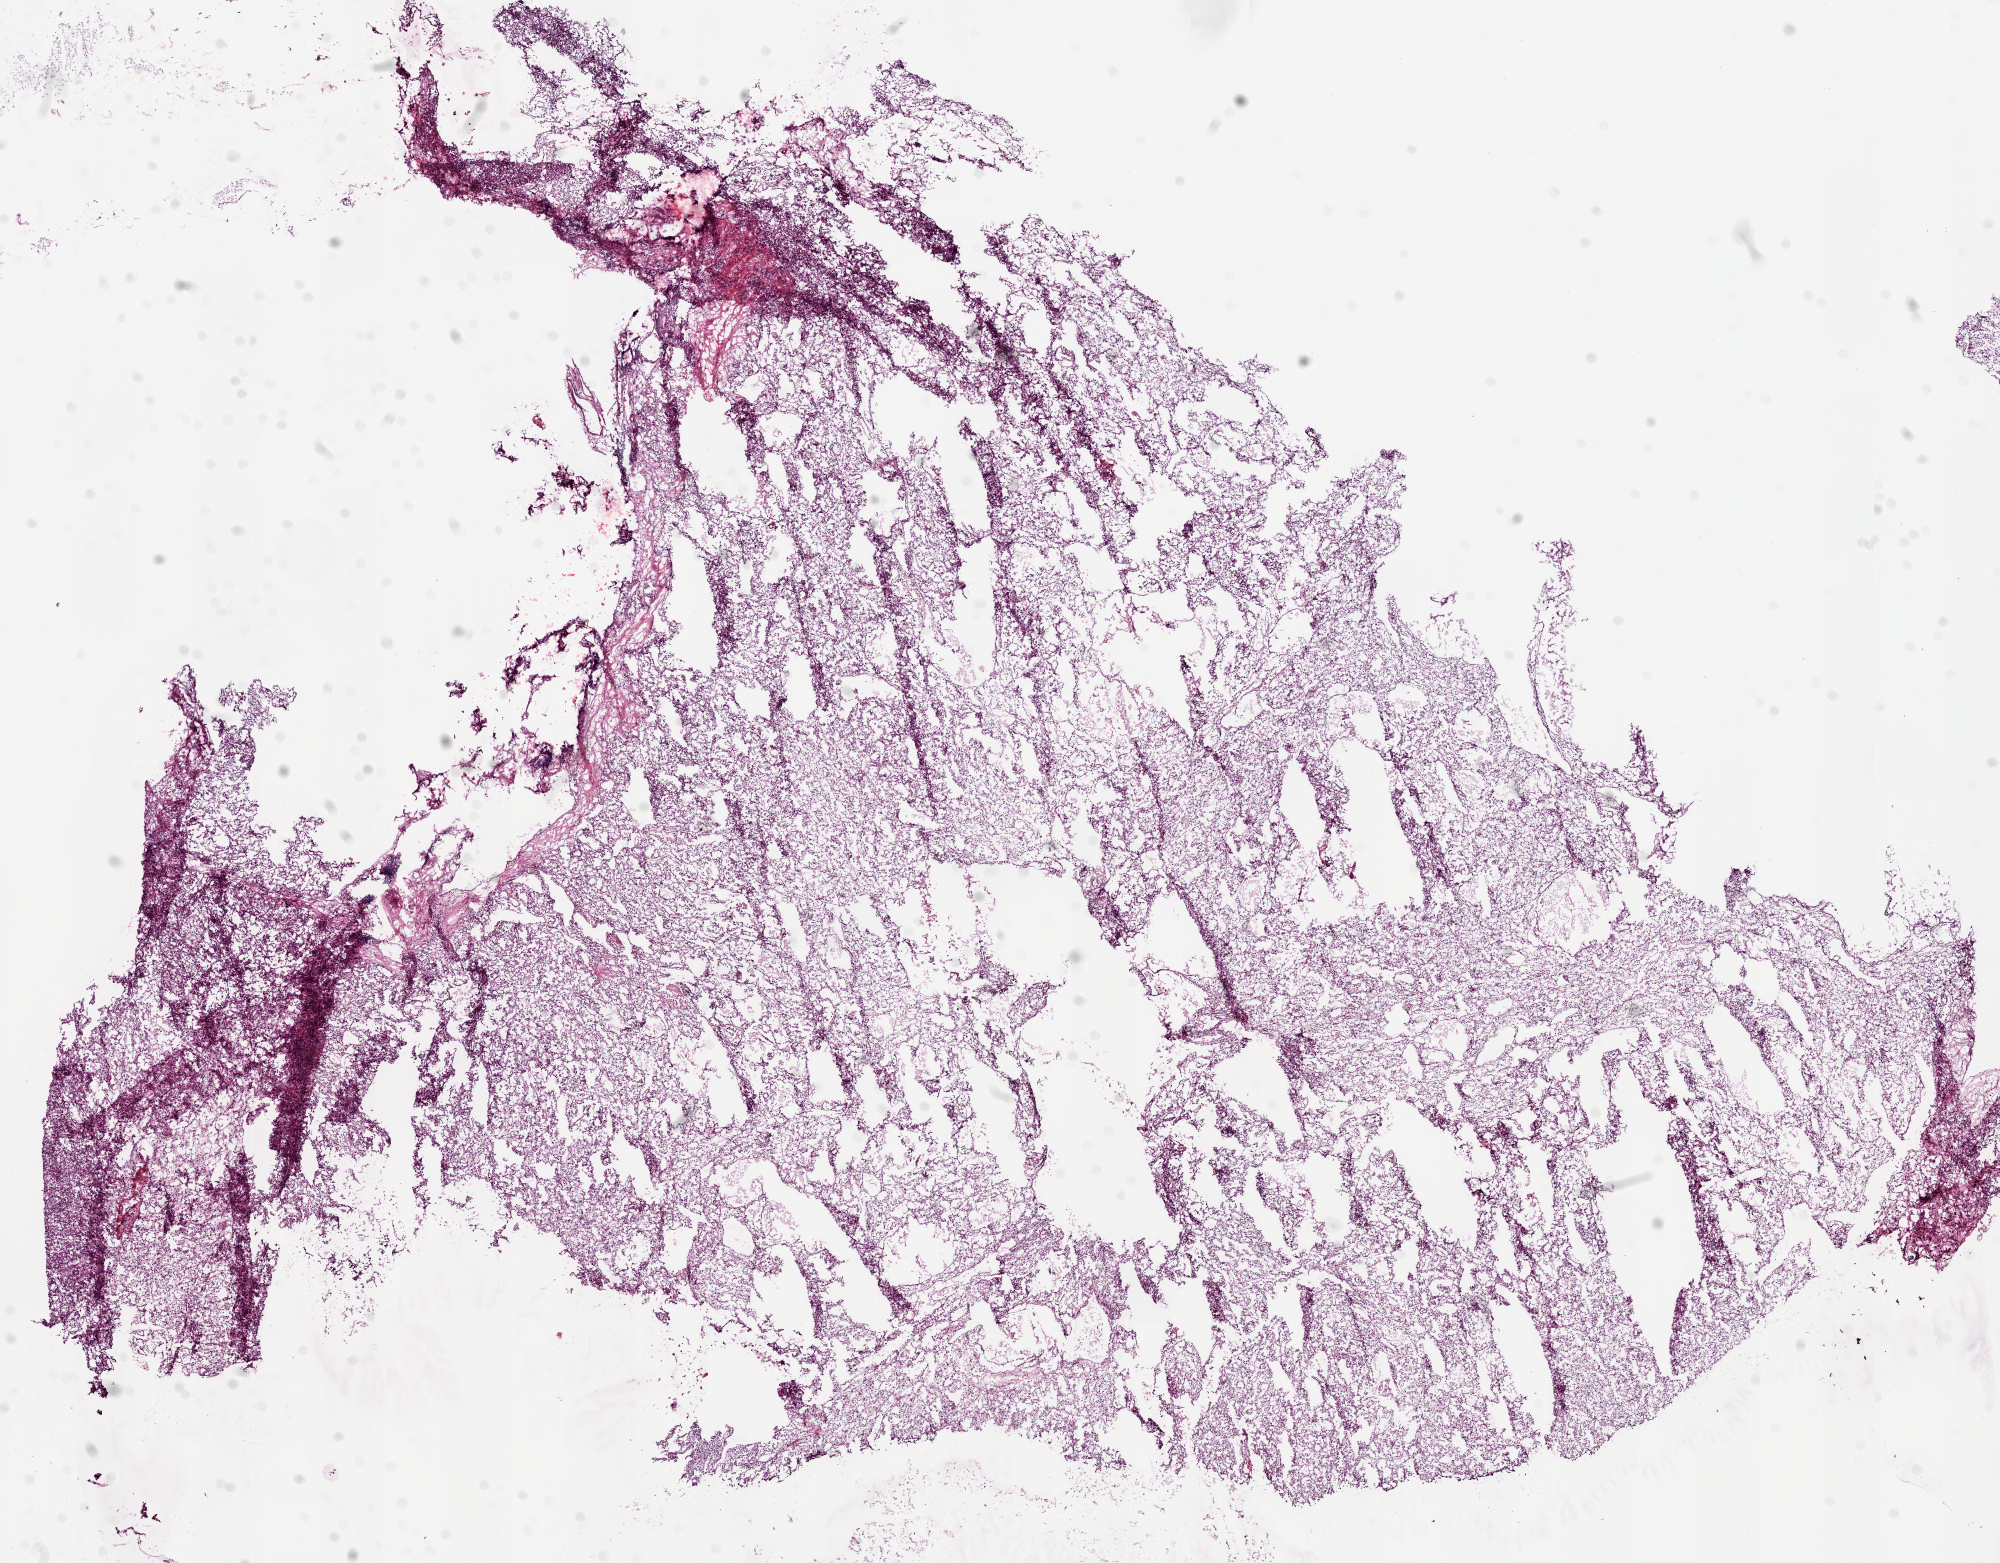
H&E whole-slide image — a low-resolution overview of the entire scanned area, about 16.0 x 12.5 mm (from a 20x scan); frozen section from the bottom of the tissue portion; sample: primary tumour, kidney. Female, age 75 years at initial diagnosis. Composition of this section per pathologist review: tumour cells 95%, tumour nuclei 85%.
Pathologic diagnosis: Clear cell adenocarcinoma, NOS.